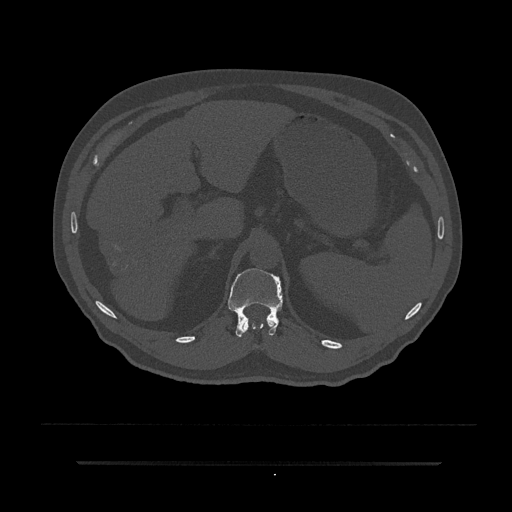
CT including the spine, one axial slice. Slice 233 of 797 in the series (ordered by position). Reconstruction kernel Br40s/3. Bone window (W 1800 / L 400 HU). 512 × 512 image matrix, field of view 464 × 464 mm. Patient: male, 59 years. From the clinical record (not read from this slice): primary cancer: bile ducts.
Outlined on this slice (semi-automatic segmentation, software-assisted and operator-edited):
- T11 vertebra: bounding box [x1, y1, x2, y2] px = [244, 318, 277, 331]
- T12 vertebra: [228, 268, 282, 337]